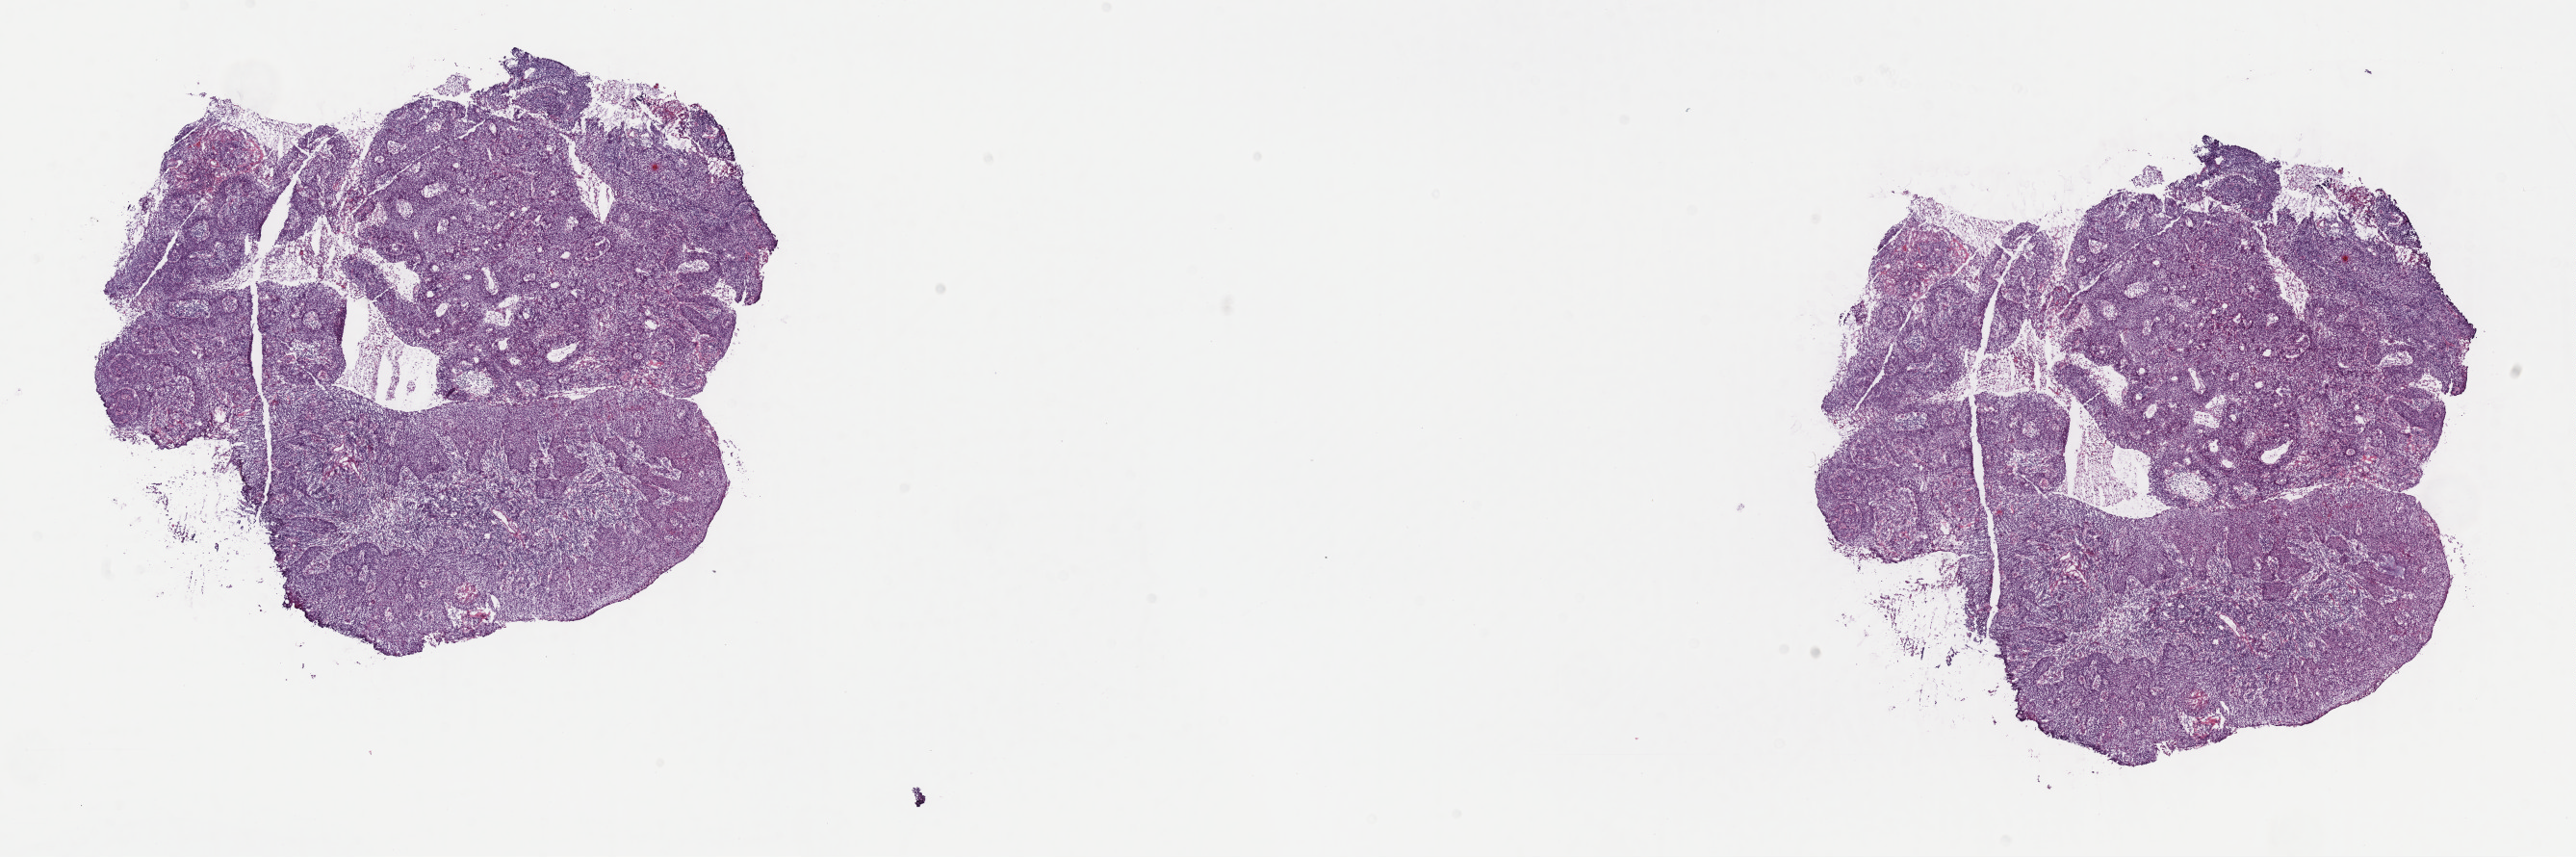
Whole-slide histology image, H&E — whole scanned area (about 21.6 x 7.2 mm, from a 40x scan) shown as a low-resolution overview; frozen section from the top of the tissue portion; sample: primary tumour, cervix. Patient: female, age at initial diagnosis 60 years. Histologic grade: G3 (poorly differentiated). Composition of this section per pathologist review: tumour cells 60%, tumour nuclei 60%, normal cells 20%, stromal cells 10%, necrosis 10%. Infiltration values recorded for this section: lymphocyte infiltration 15%, monocyte infiltration 0%, neutrophil infiltration 0%.
Histologic diagnosis: Squamous cell carcinoma, NOS (cervix uteri). FIGO stage: IIIA.